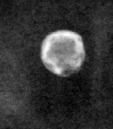
Cropped region of a digitized screen-film mammogram centred on a radiologist-marked abnormality, right breast, CC view, BI-RADS breast density category 1 (scale 1–4).
- Marked abnormality: calcifications, morphology lucent center; BI-RADS assessment category 2; benign without callback (not worked up further).